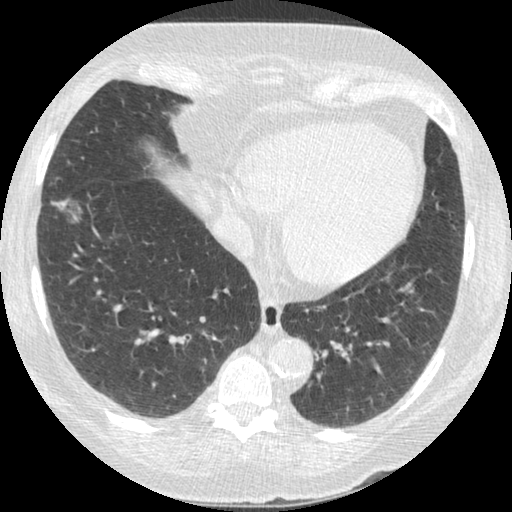
Low-dose screening chest CT, one axial slice. Position 93 of 245 along the scan axis. Reconstruction kernel STANDARD. Lung window (W 1500 / L -600 HU). 512 × 512 image matrix, field of view 310 × 310 mm.
Outlined on this slice (expert manual segmentation):
- lesion 1 (tumor, lower lobe of right lung): bounding box [x1, y1, x2, y2] px = [52, 197, 83, 222]